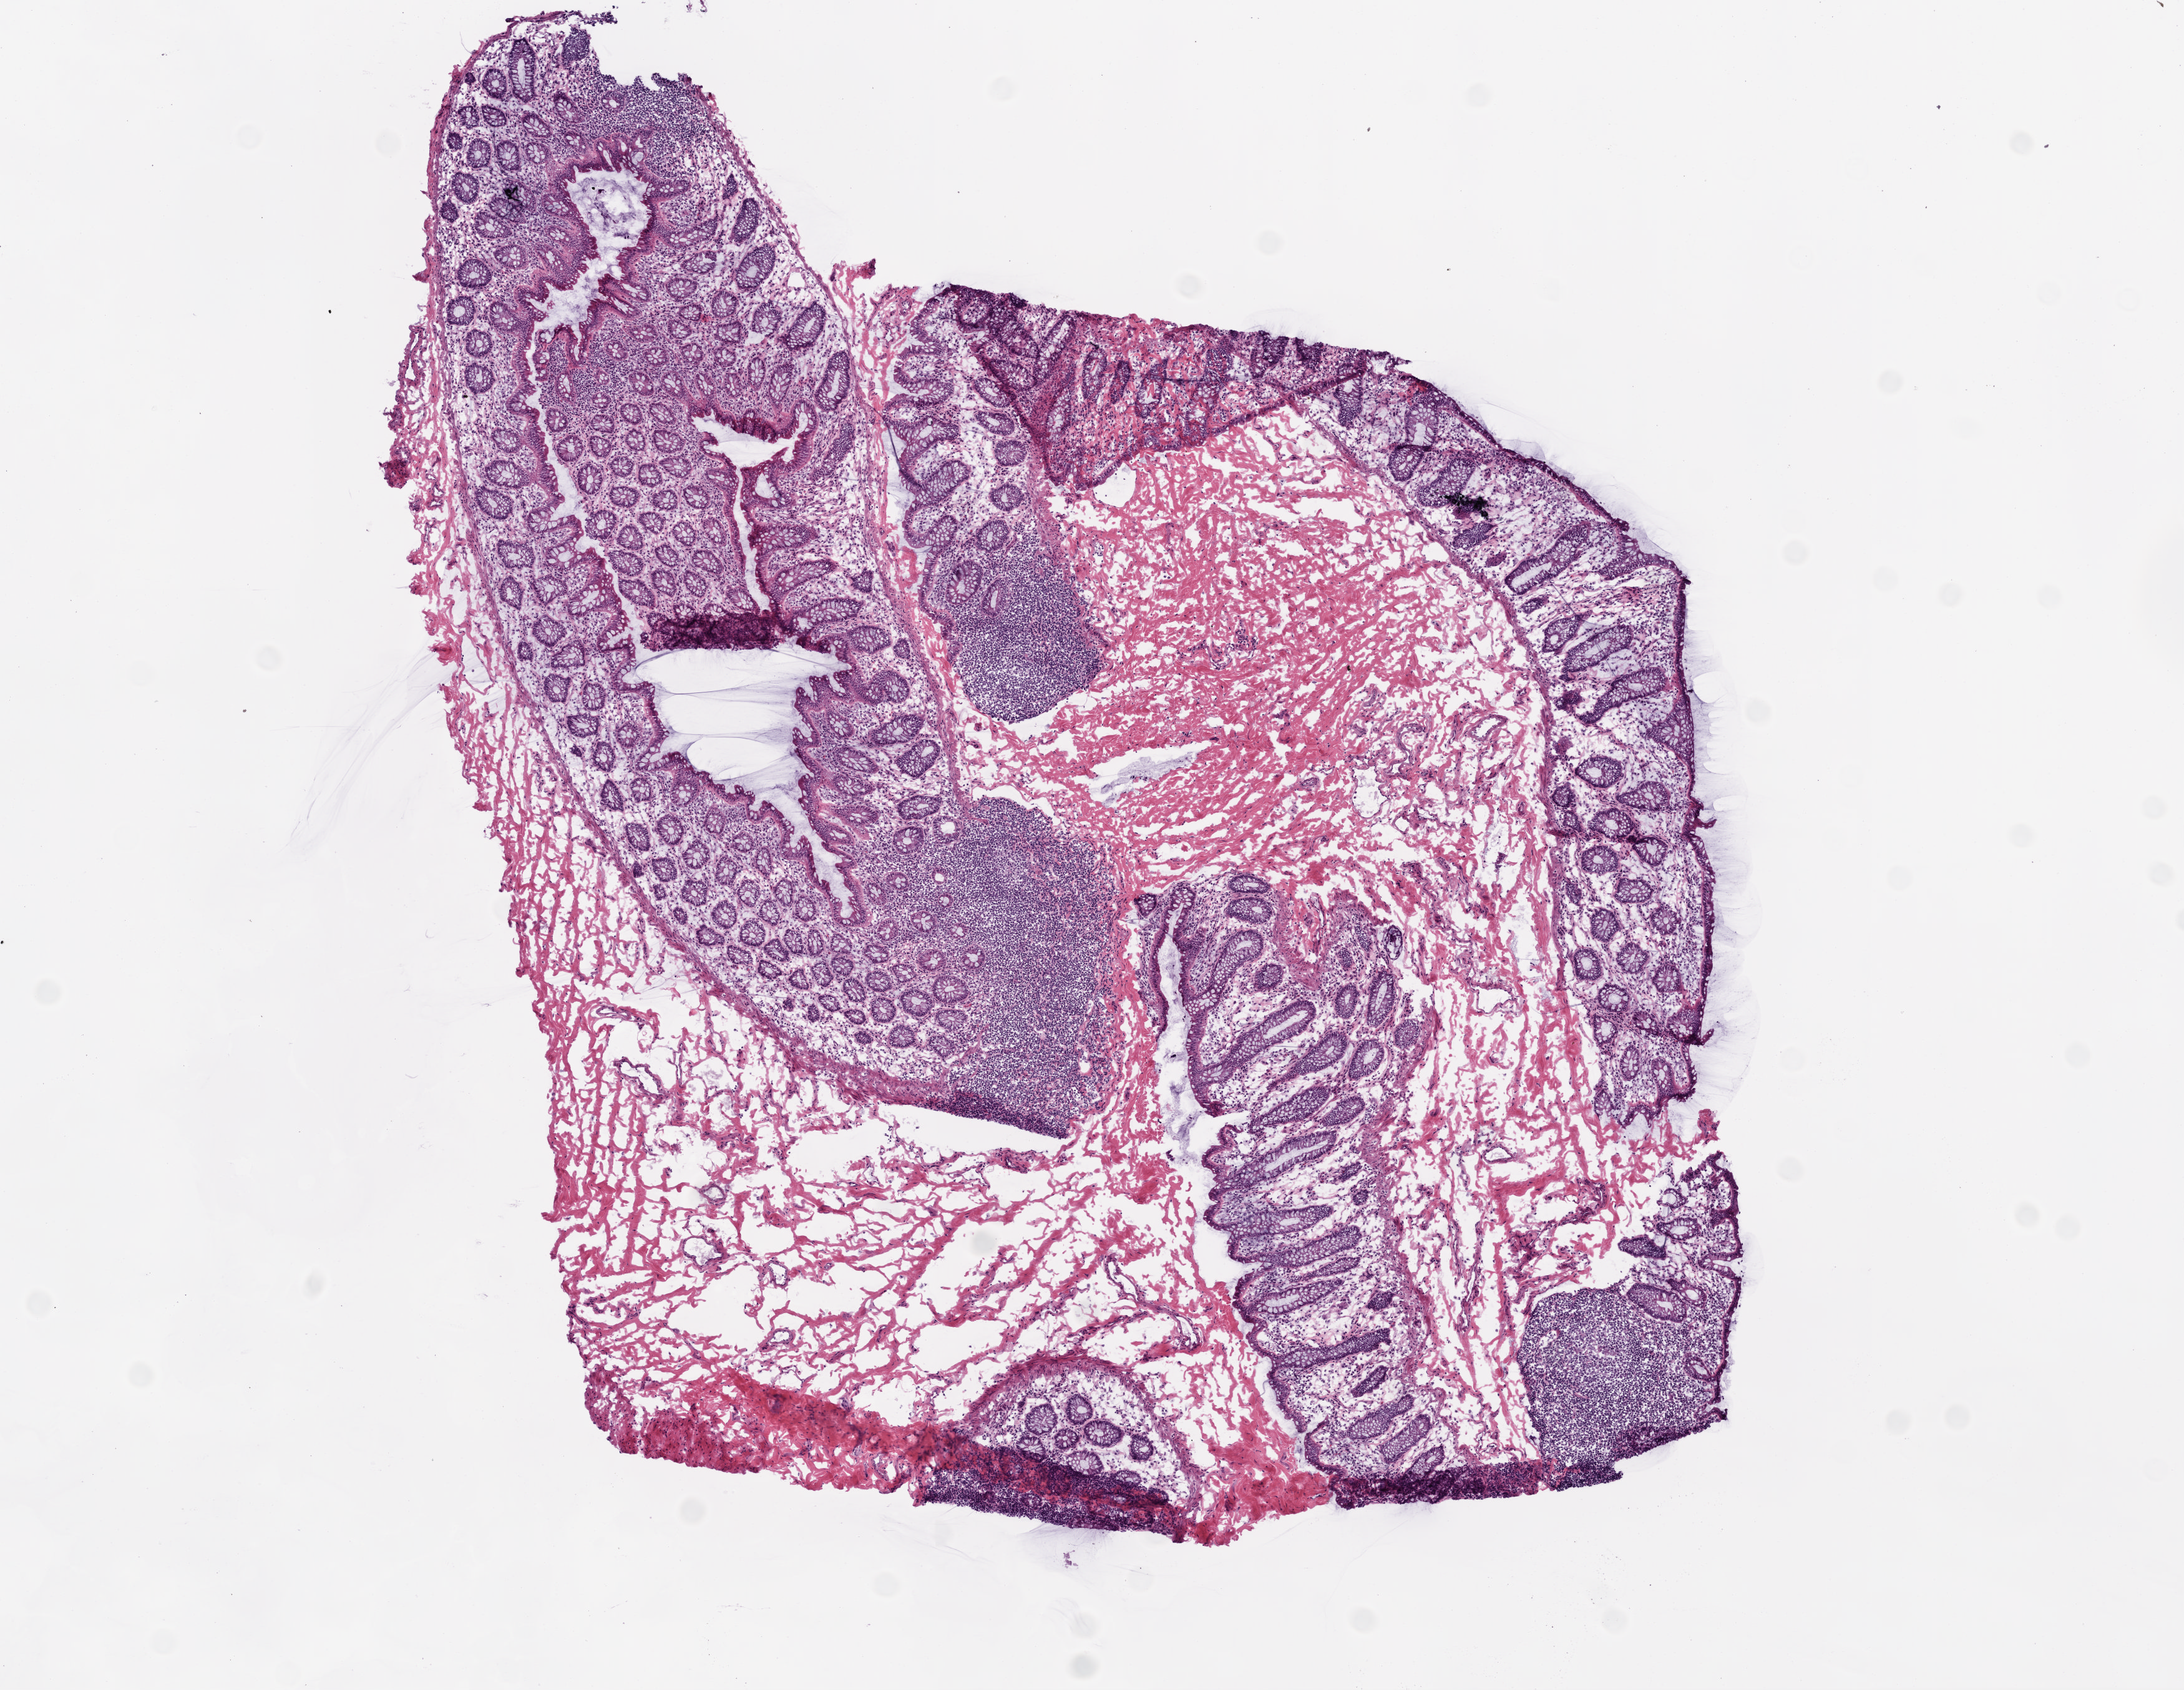
Hematoxylin and eosin (H&E) stained whole-slide image, low-resolution overview of the scanned area, about 7.0 x 5.4 mm (slide scanned at 20x). Frozen section from the top of the tissue portion. Solid tissue normal (non-tumour tissue) sample from the colon. Male, age 63 years at initial diagnosis.
* this section: solid tissue normal sample (biorepository sample class)
* patient diagnosis: Adenocarcinoma, NOS